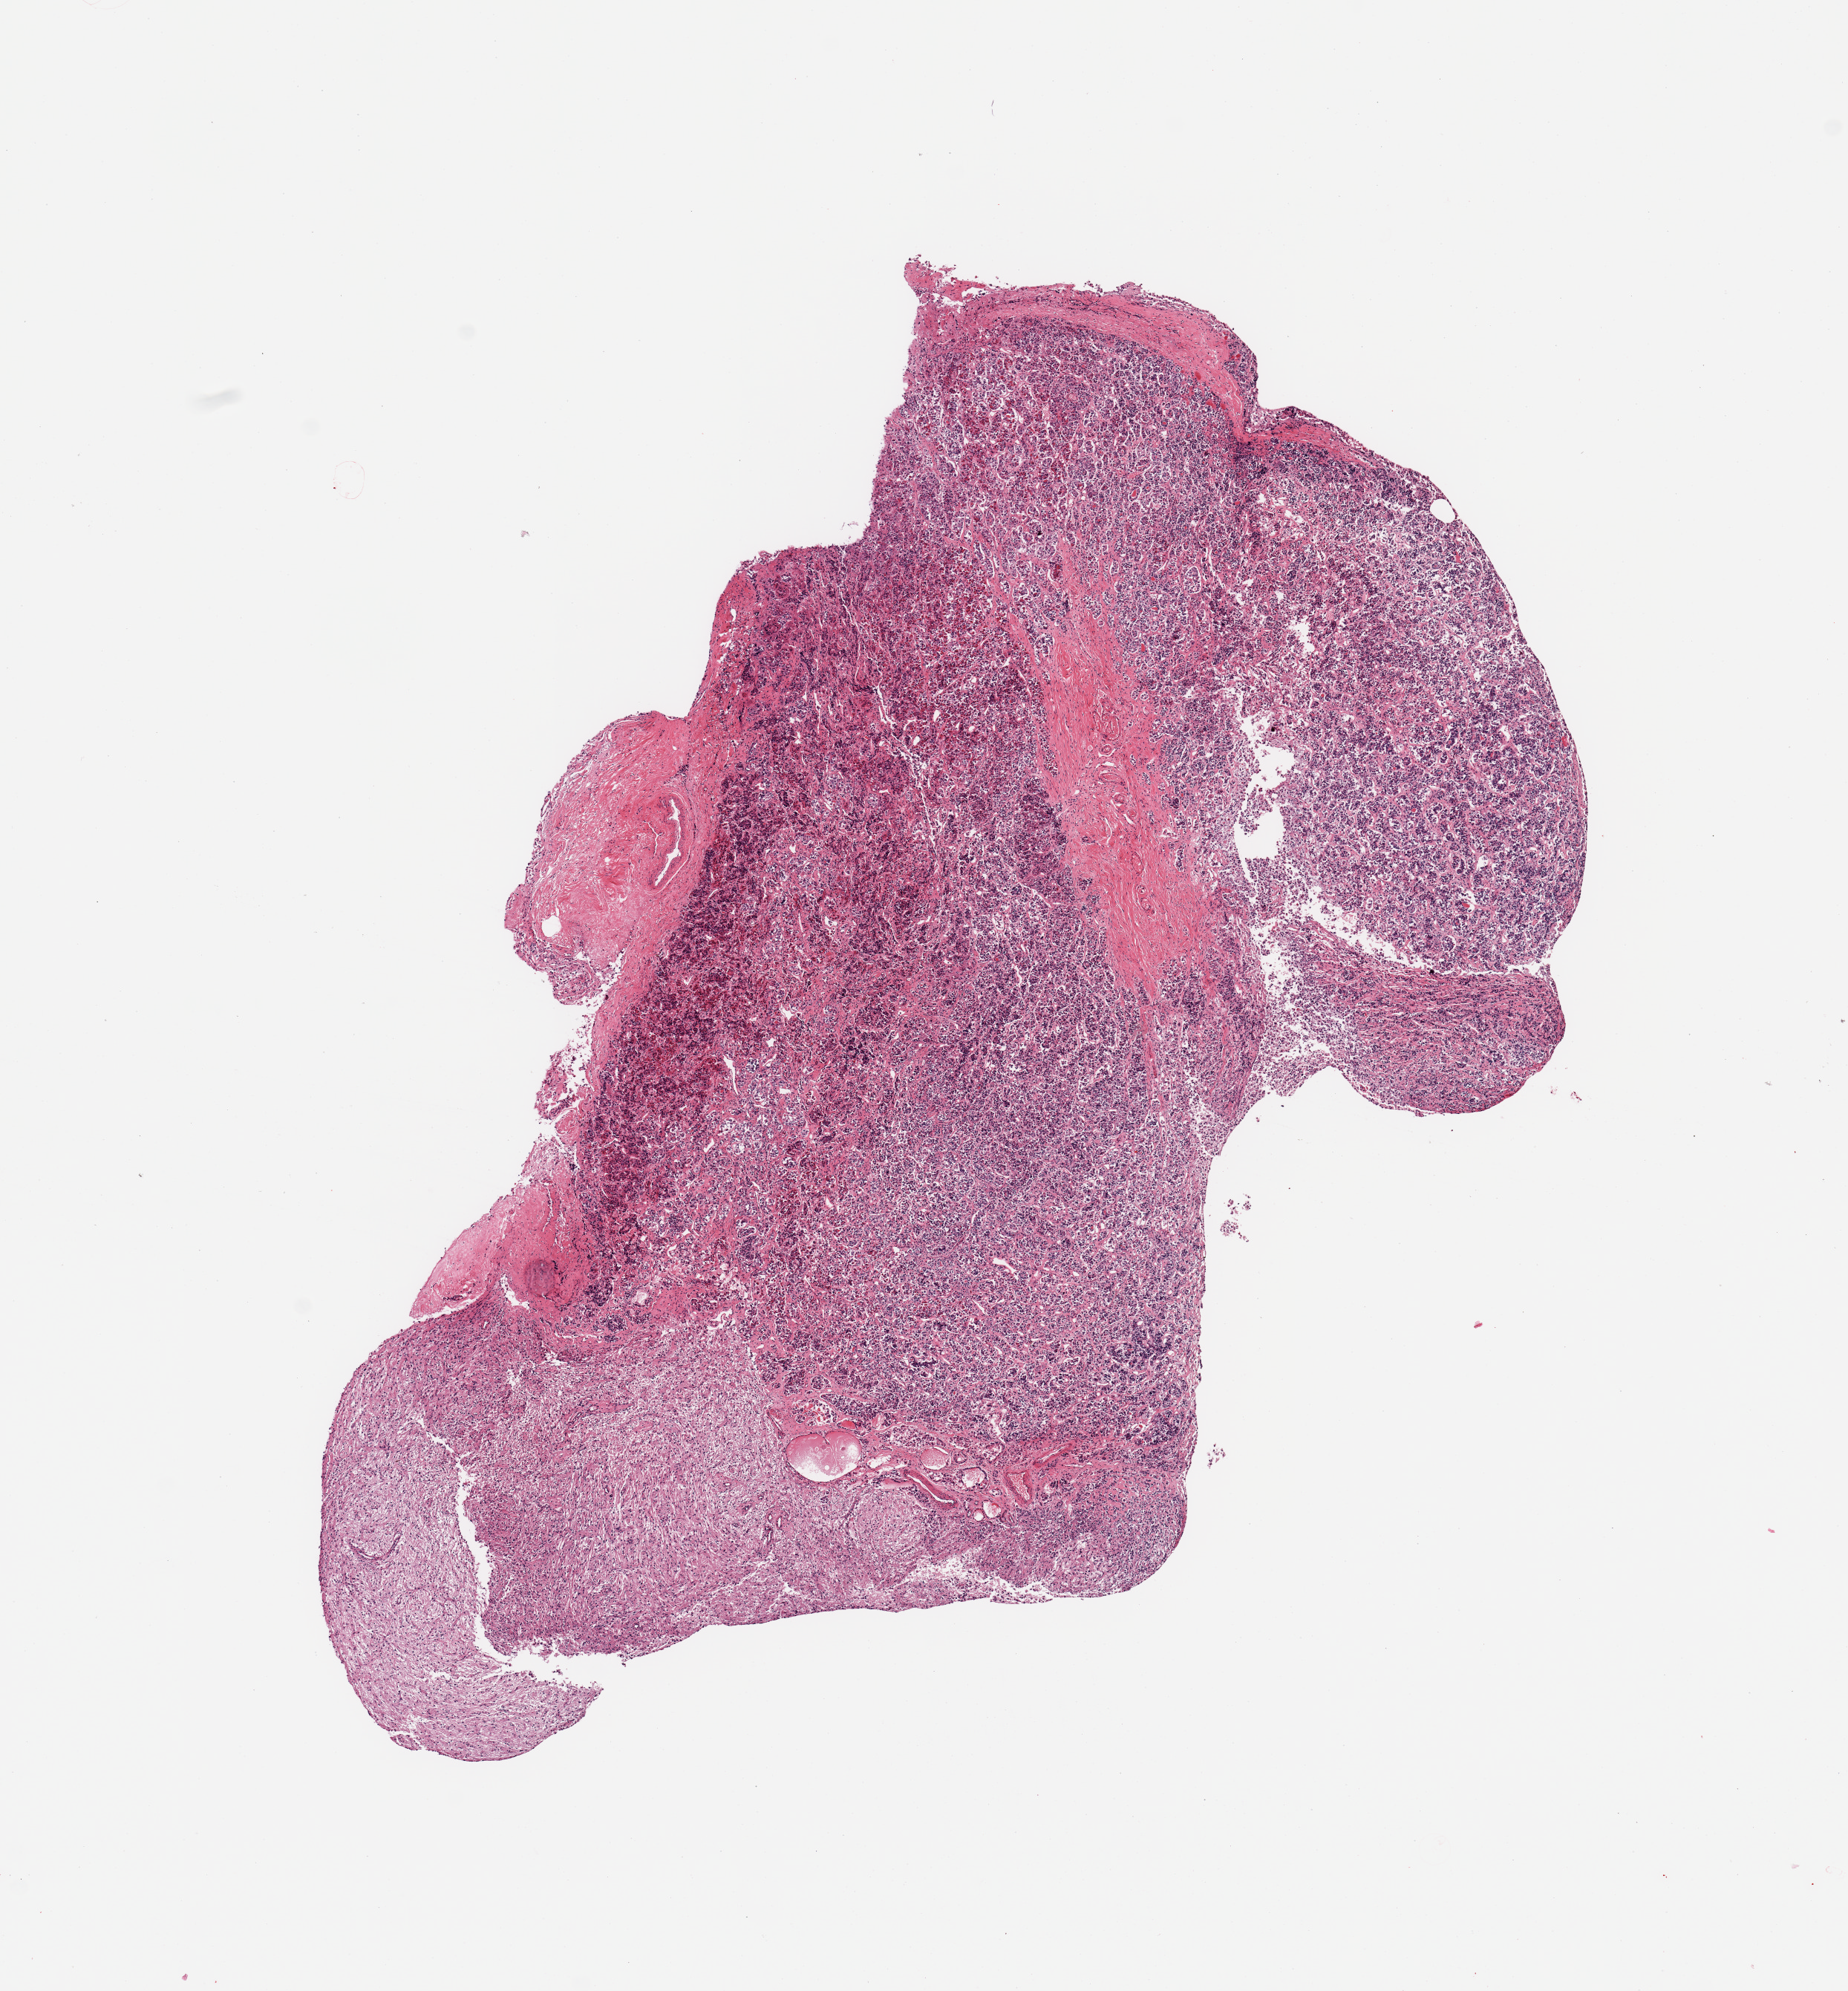
Whole-slide image, H&E stain, brightfield, low-resolution overview of the scanned area, about 9.8 x 10.6 mm (slide scanned at 20x); PAXgene-fixed paraffin-embedded (PFPE) section; sampled site (target tissue): pituitary; donor tissue sample. Male donor.
Pathologist's review note for this sample: 1 piece; adenohypophysis and neurohypophysis.